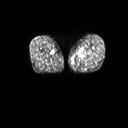
FDG PET of an extremity soft-tissue mass (from a PET/CT study), one axial slice; position 9 of 267 along the scan axis; 3.27 mm slice thickness; 128 × 128 image matrix. Patient: male, 59 years. Case-level facts recorded for this patient, not image findings: histological type: pleiomorphic liposarcoma; grade: high; site of the primary tumour: left thigh.
Outlined on this slice (expert contour drawn on MRI and transferred to this co-registered scan by the dataset authors):
- gross tumour volume including surrounding oedema: bounding box (x1, y1, x2, y2) in pixels: (78, 52, 88, 59)